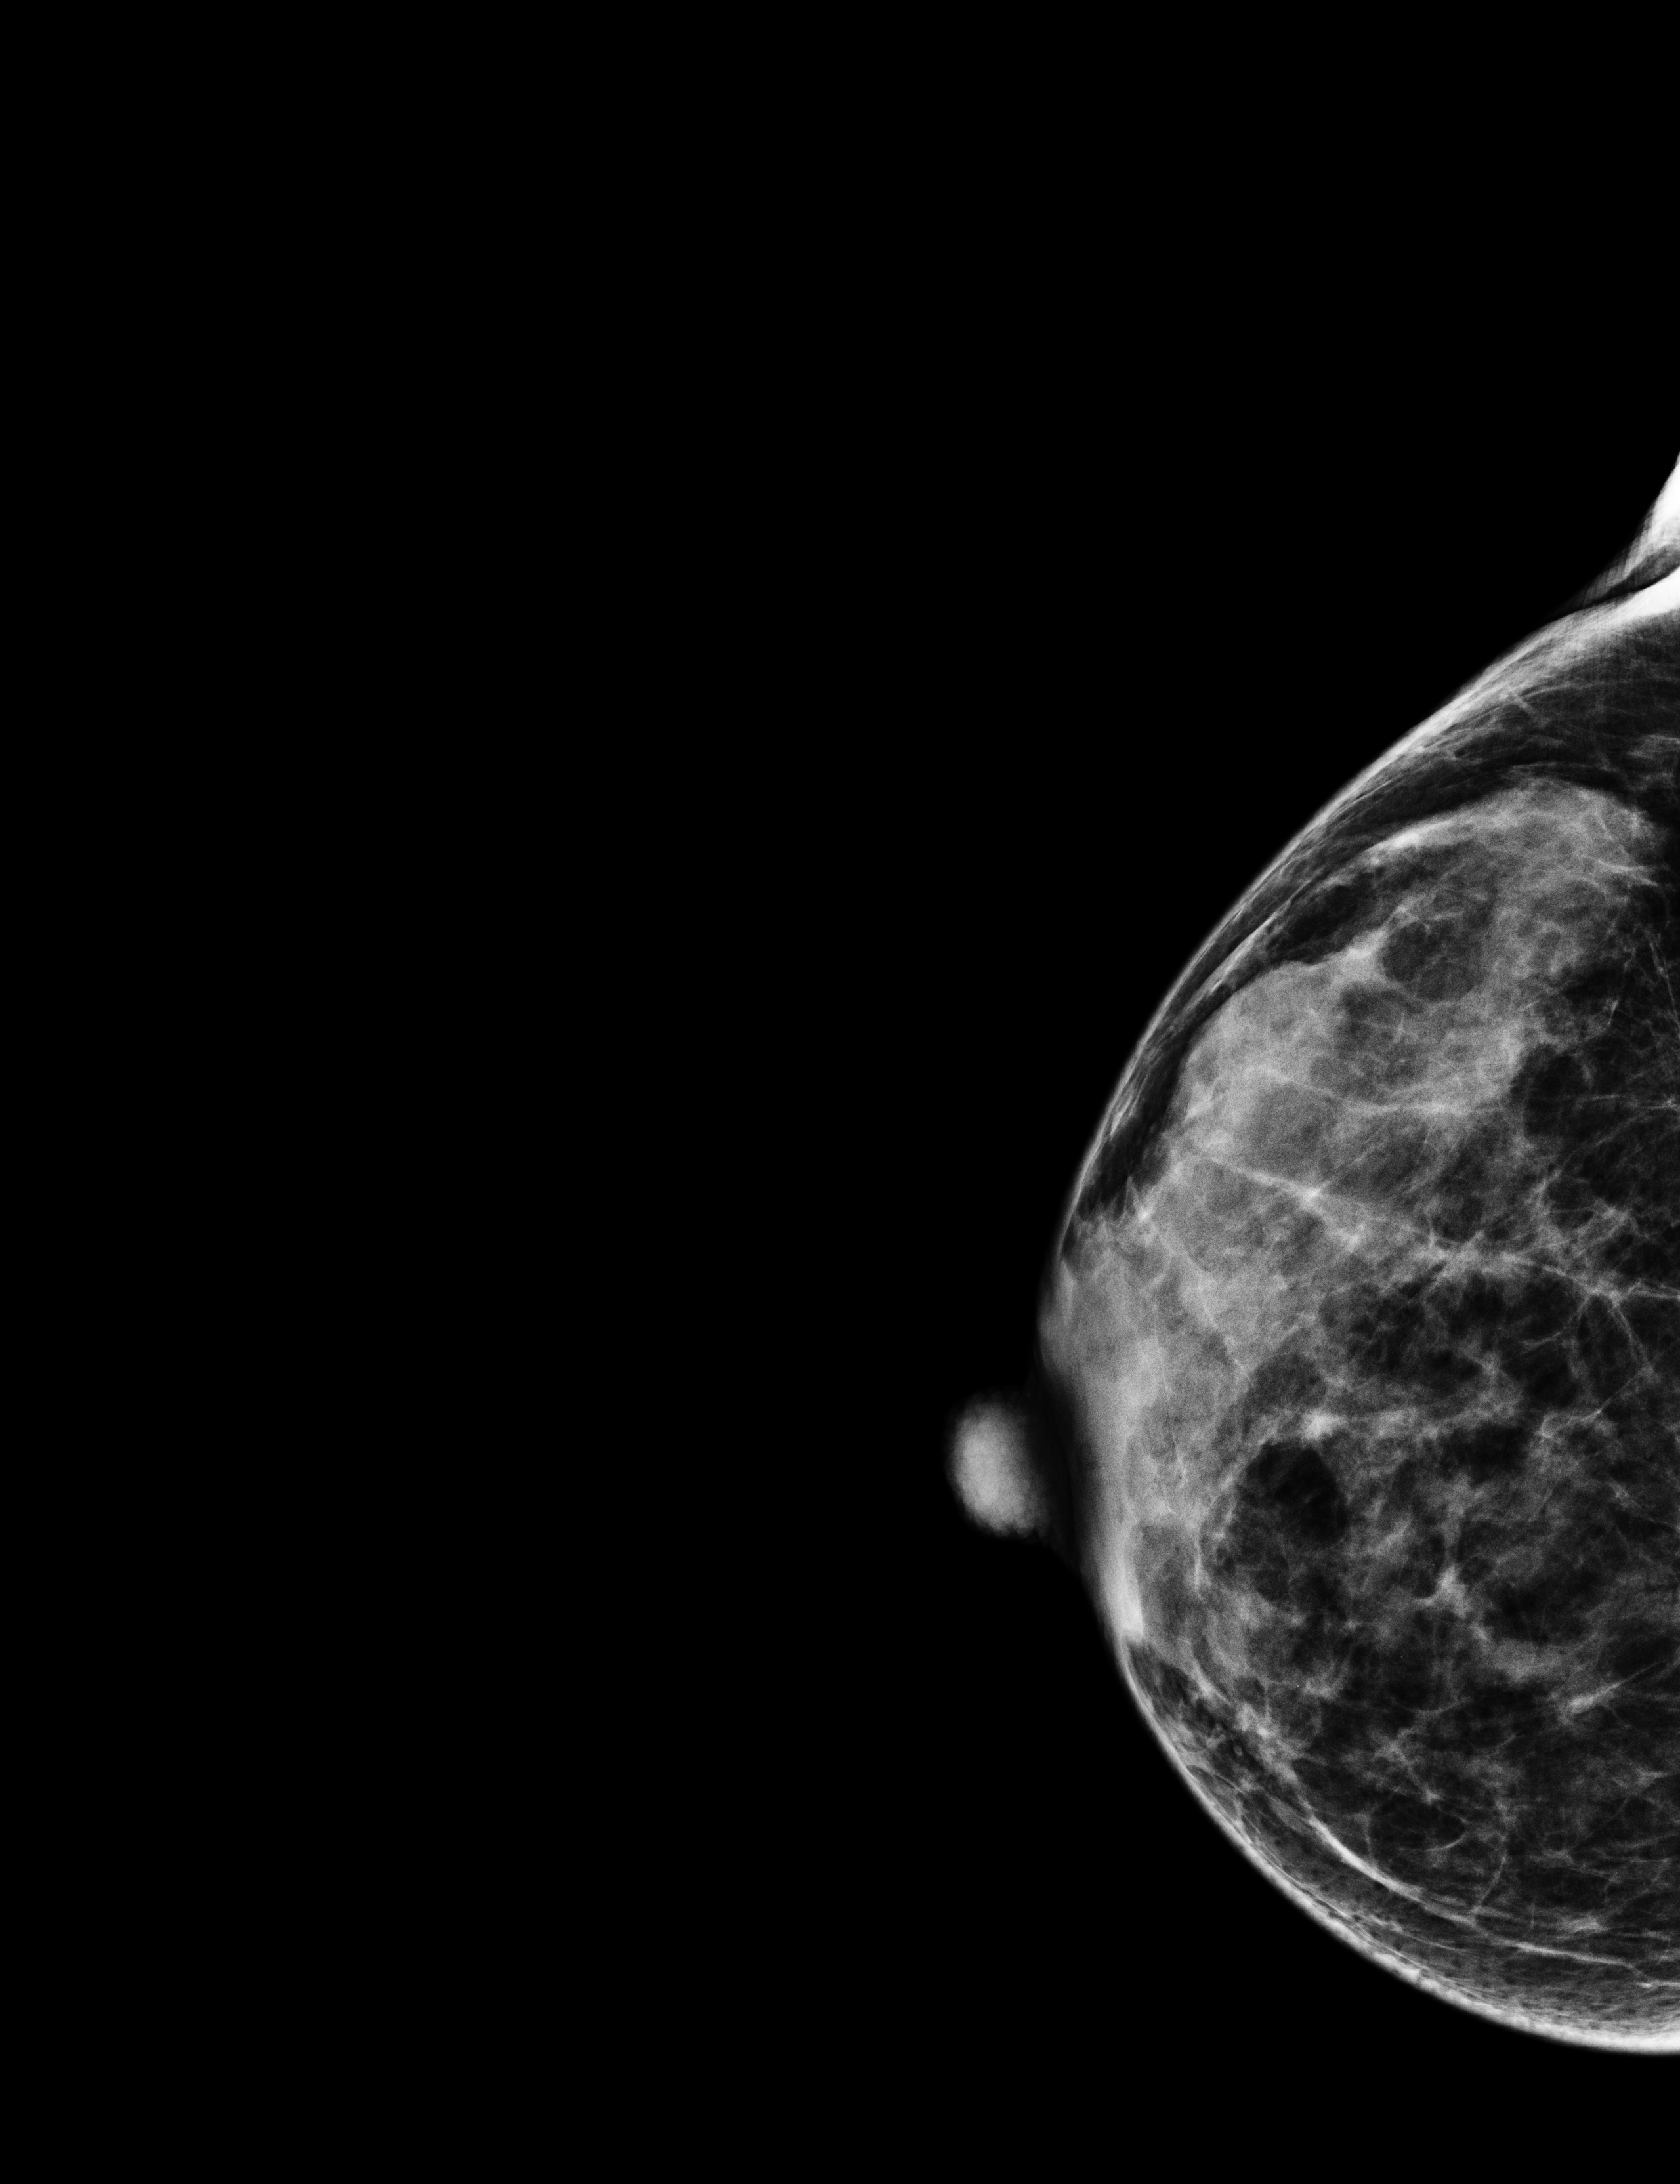
Annual screening mammography examination; compressed breast thickness 34 mm. Patient aged 50 years (female).
Image type: full-field digital mammogram. Breast: right. Projection: exaggerated CC view (lateral).